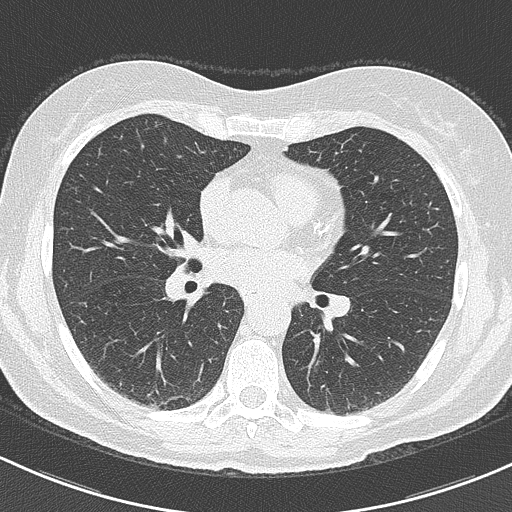
Low-dose screening chest CT, one axial slice. Slice 104 of 201 in the series (ordered by position). Reconstruction kernel B70f. Lung window (W 1500 / L -600 HU). 2 mm slice thickness. 512 × 512 image matrix, field of view 312 × 312 mm.
Annotated regions visible in this slice (manually delineated by an expert):
- lesion 1 (tumor, upper lobe of right lung): bounding box <79,302,87,307> (left, top, right, bottom; pixels)